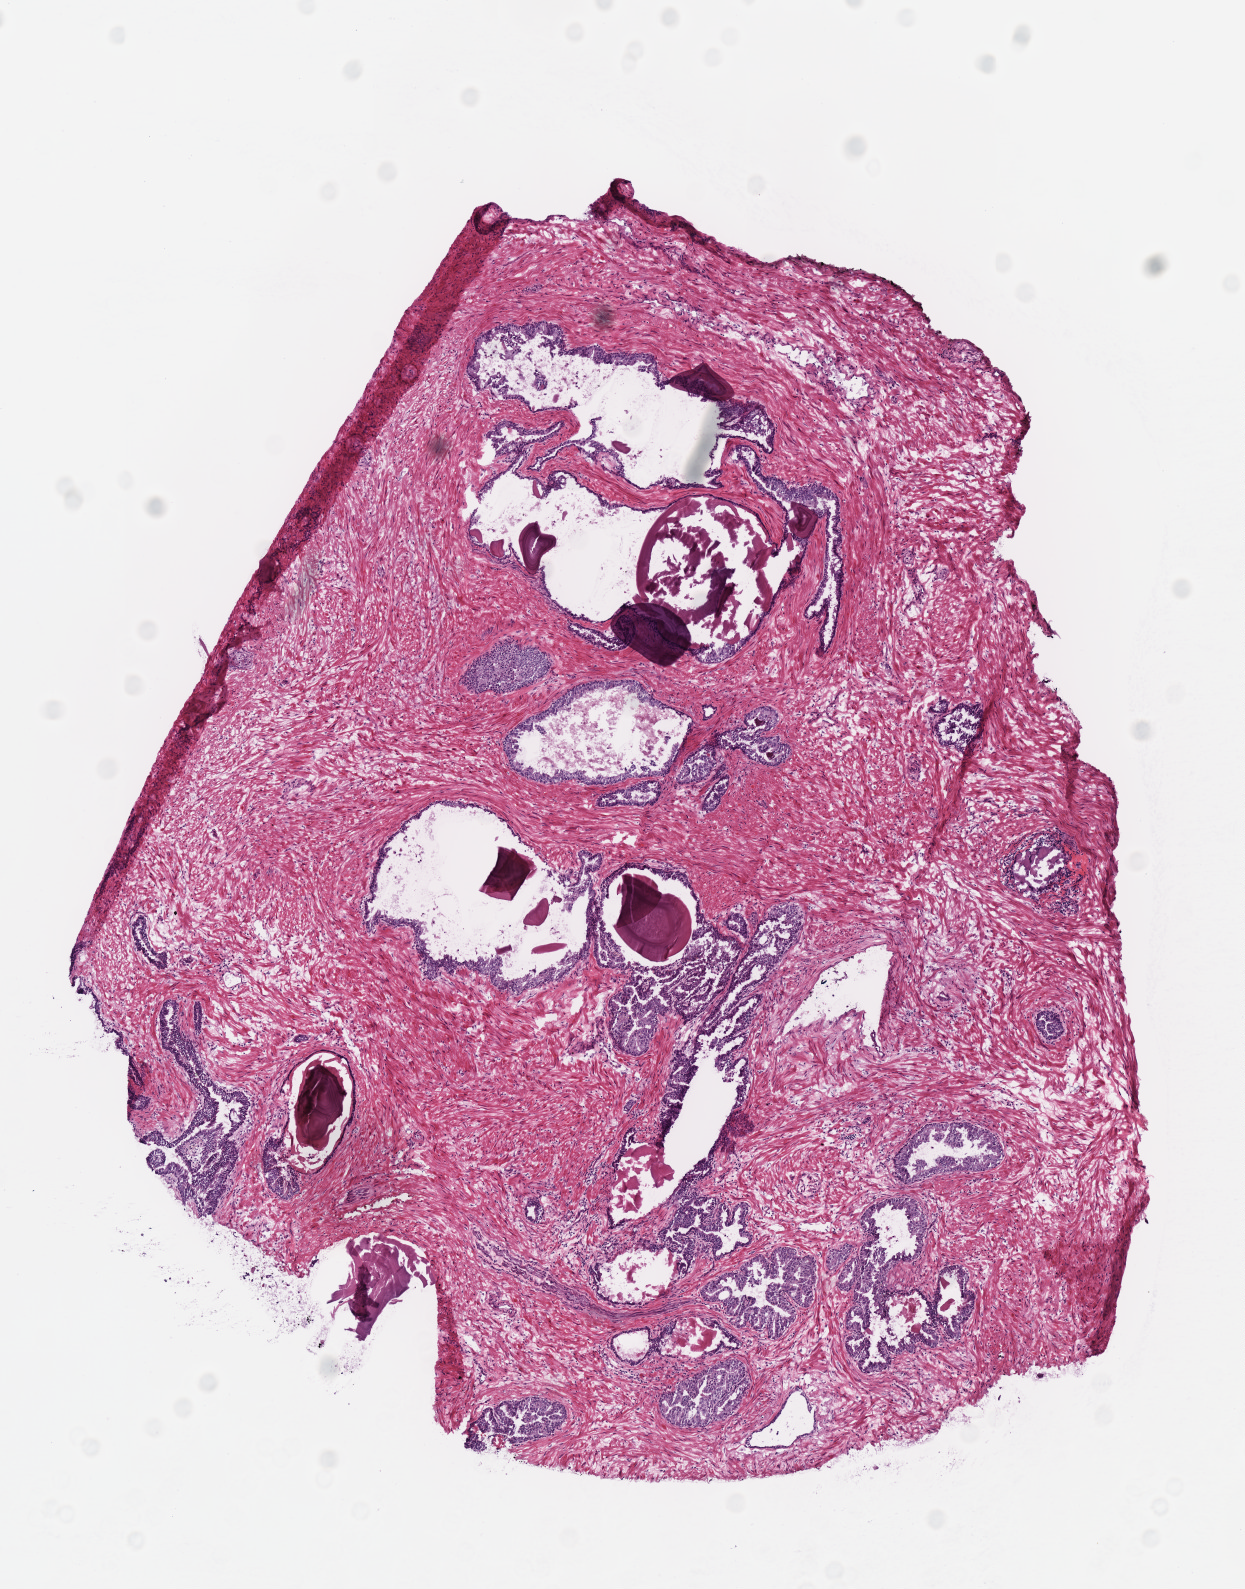
Whole-slide histology image, Hematoxylin and eosin (H&E) stained, whole scanned area (about 4.9 x 6.2 mm) shown as a low-resolution overview, frozen section from the top of the tissue portion, prostate, solid tissue normal (non-tumour tissue) sample. Male patient; age at initial diagnosis 58 years.
- this section: solid tissue normal sample (biorepository sample class)
- patient diagnosis: Adenocarcinoma, NOS (prostate gland)